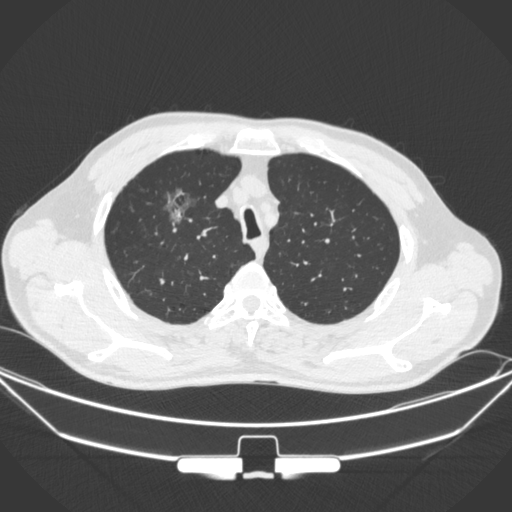
Chest CT, one axial slice. 120 kVp. Lung window (W 1500 / L -600 HU). 512 × 512 image matrix, field of view 399 × 399 mm. Male patient, age 67 years. Case-level facts recorded for this patient, not image findings: clinical TNM (as recorded): T1c N0 M0; histopathological grade: G2.
Annotated regions visible in this slice (bounding box drawn by a radiologist):
- lung tumour (recorded histology: adenocarcinoma): bounding box <161,182,208,232> (left, top, right, bottom; pixels)